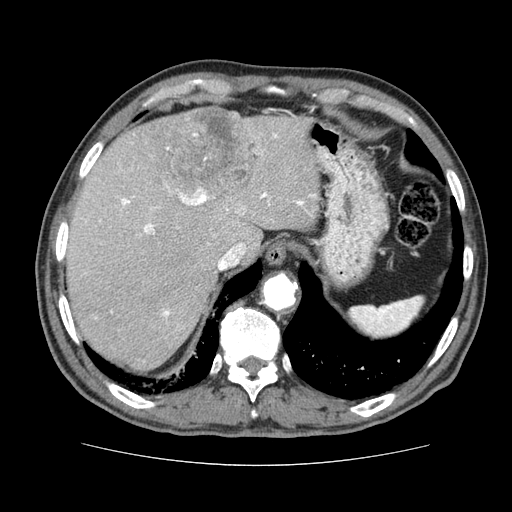
Contrast-enhanced abdominal CT (liver protocol), one axial slice; slice 59 of 79 in the series (ordered by position); 120 kVp; soft-tissue window (W 400 / L 40 HU); 2.5 mm slice thickness; 512 × 512 image matrix. Case-level facts recorded for this patient, not image findings: diagnosis: hepatocellular carcinoma (patient treated with transarterial chemoembolisation; whether this scan precedes or follows treatment is not stated here); TNM stage (as recorded): Stage-I; Child-Pugh class: A; tumour nodularity: uninodular.
Structures marked on this image (semi-automatic segmentation, software-assisted and operator-edited):
- liver parenchyma outside the tumour (the mass and vessels are separate outlines, so this box may not span the whole liver): box from (x=66, y=112) to (x=320, y=370) px
- mass: (x=143, y=107)–(x=259, y=207)
- liver vessels: (x=111, y=133)–(x=315, y=317)